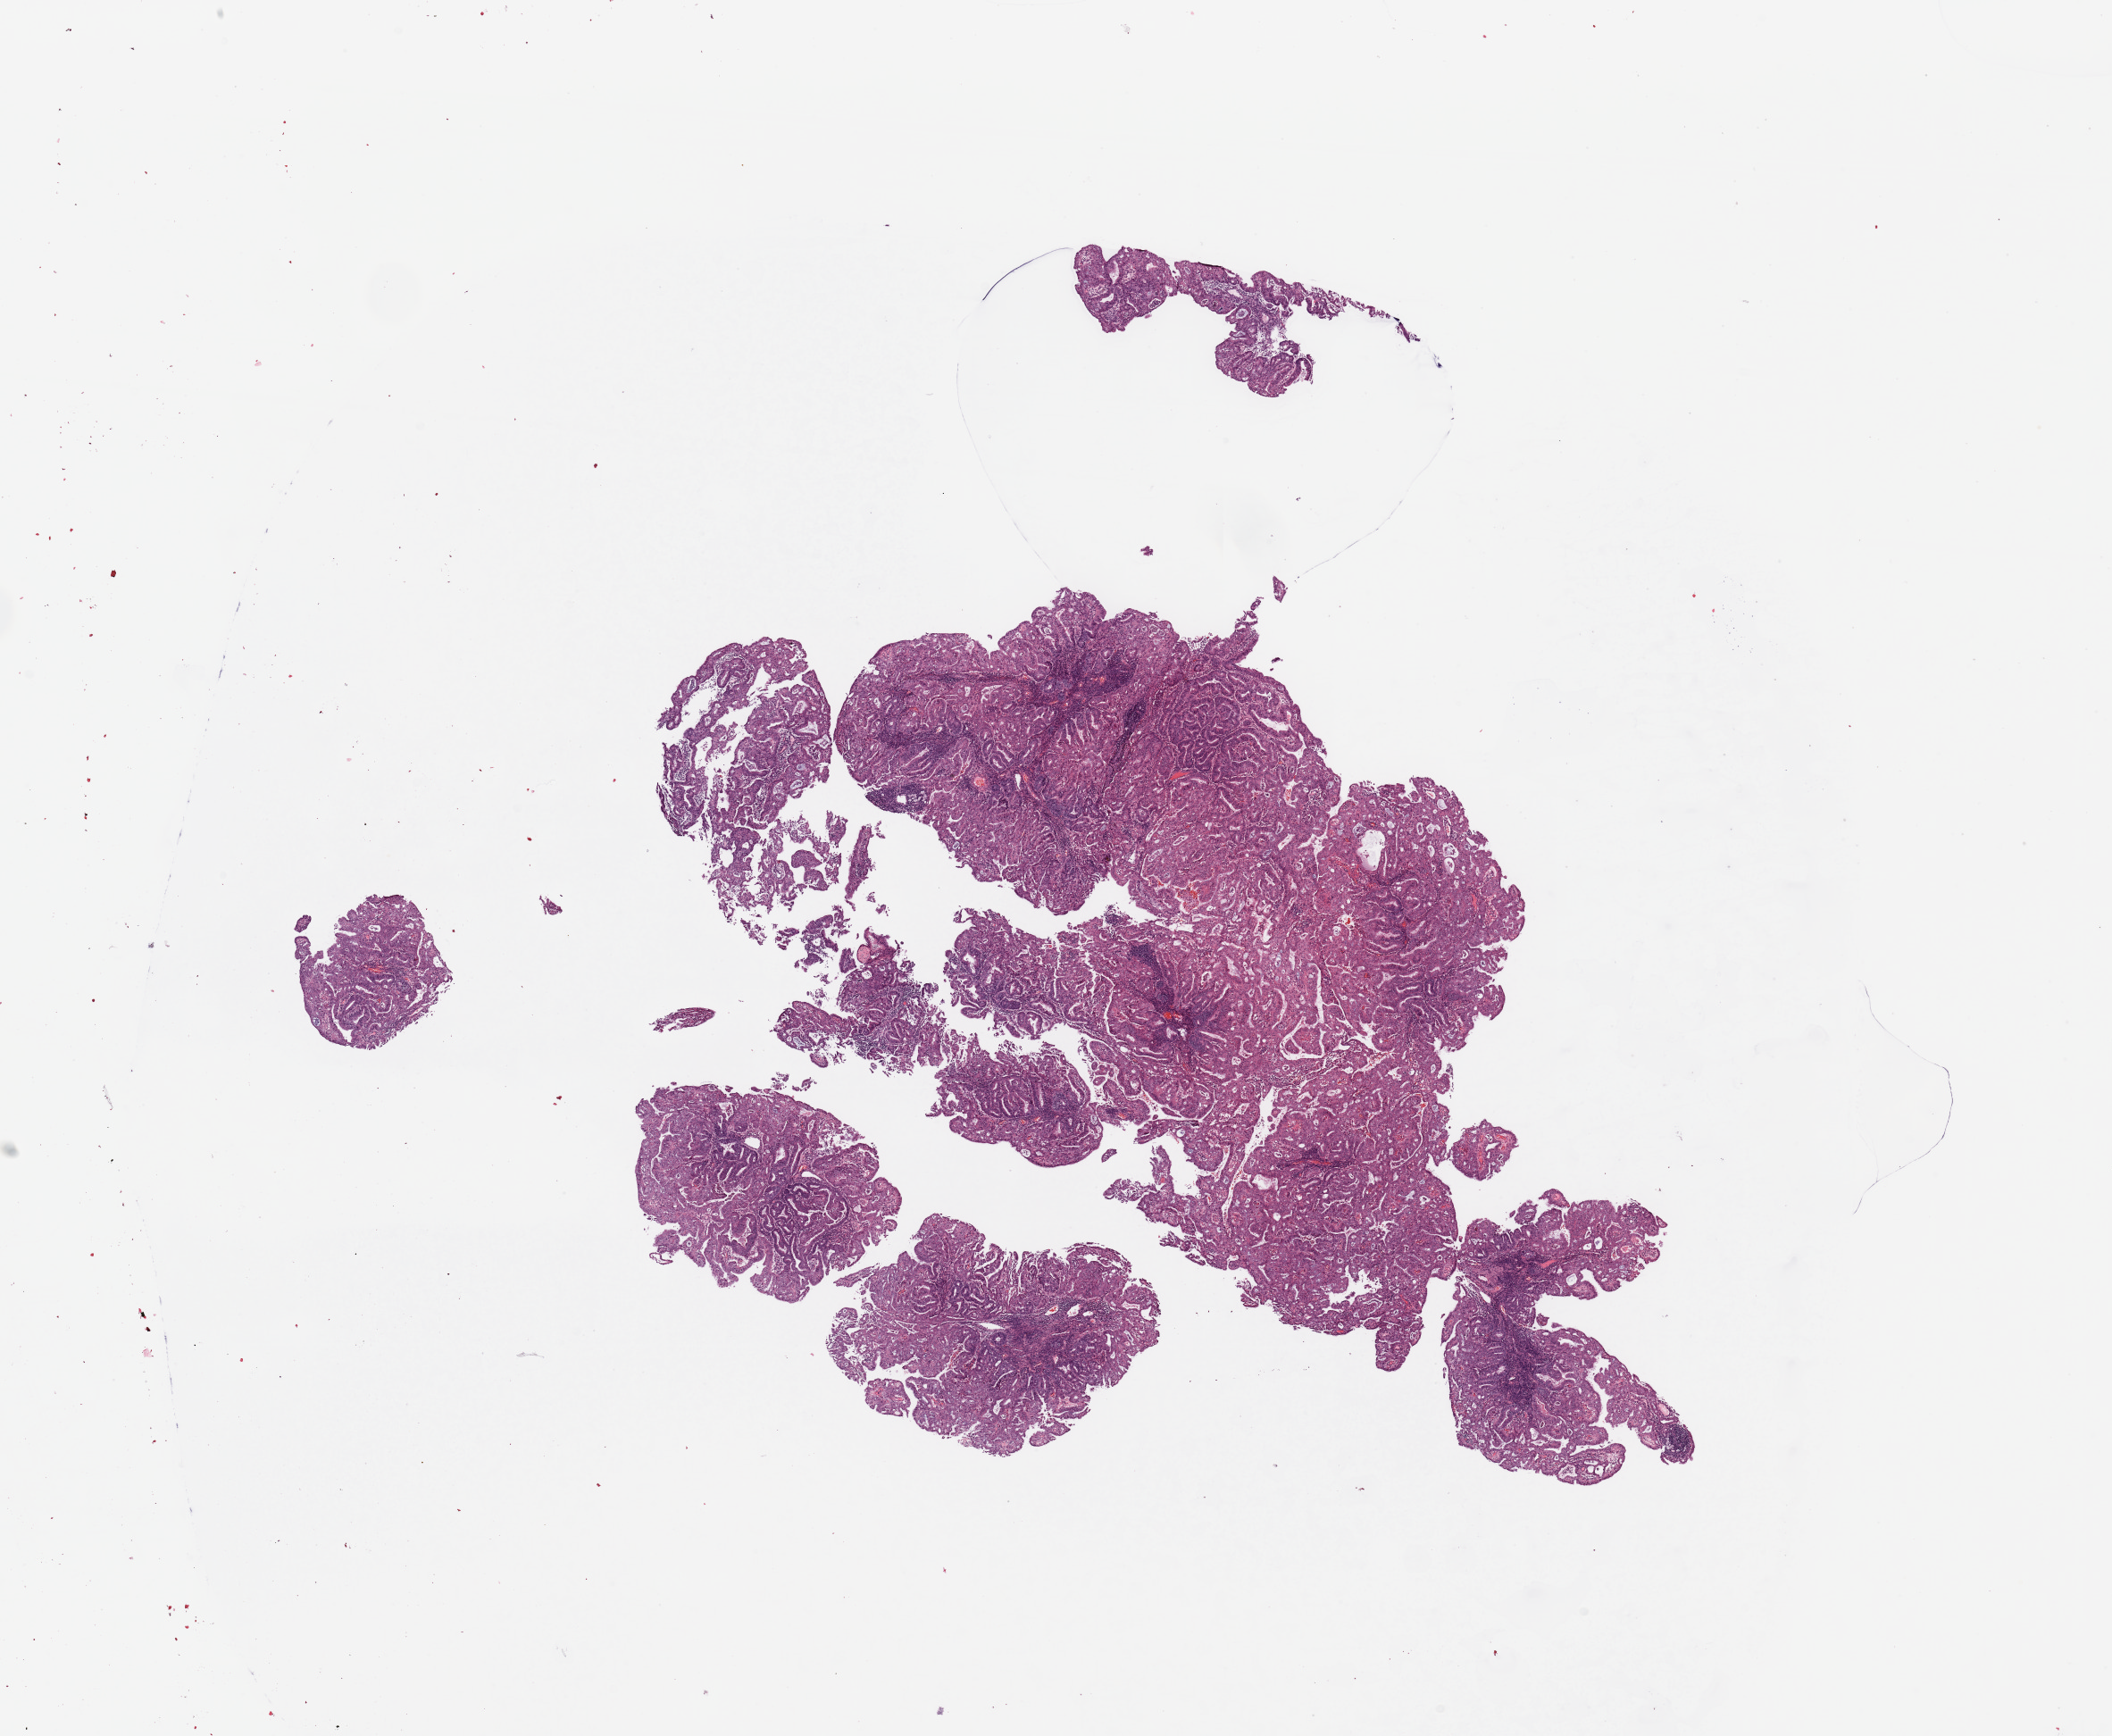
H&E whole-slide image, shown as a low-resolution overview of the whole scanned area (about 18.7 x 15.4 mm, from a 20x scan), tumour tissue sample, sampled site: uterus. 62-year-old female patient. Histologic grade: G2 (moderately differentiated). Composition of this section per pathologist review: tumour nuclei 90%, necrosis 0%.
* AJCC pathologic stage: IIIC1
* diagnosis: Endometrioid adenocarcinoma, NOS